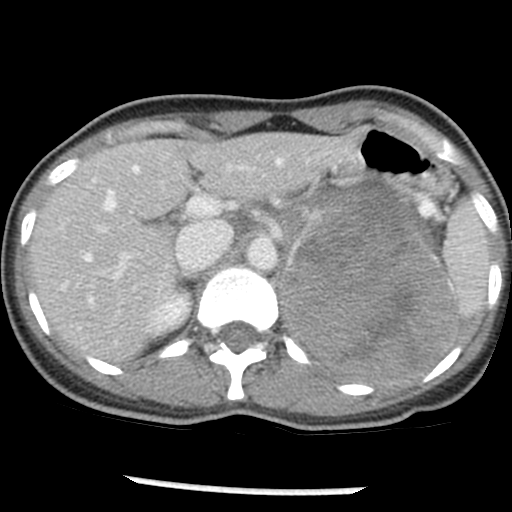
Contrast-enhanced abdominal CT, one axial slice. Slice 32 of 54 in the series (ordered by position). Reconstruction kernel STANDARD. 120 kVp. Intravenous contrast given. Soft-tissue window (W 400 / L 40 HU). 5 mm slice thickness. 512 × 512 image matrix, field of view 240 × 240 mm. Patient: female, 33 years. Case-level facts recorded for this patient, not image findings: diagnosis: adrenocortical carcinoma; tumour side: left adrenal; tumour size at pathology: 11 cm; Ki-67 index: 20 %; stage (as recorded): 2.
Structures marked on this image (semi-automatically segmented with operator editing):
- mass: bounding box <282,186,458,382> (left, top, right, bottom; pixels)